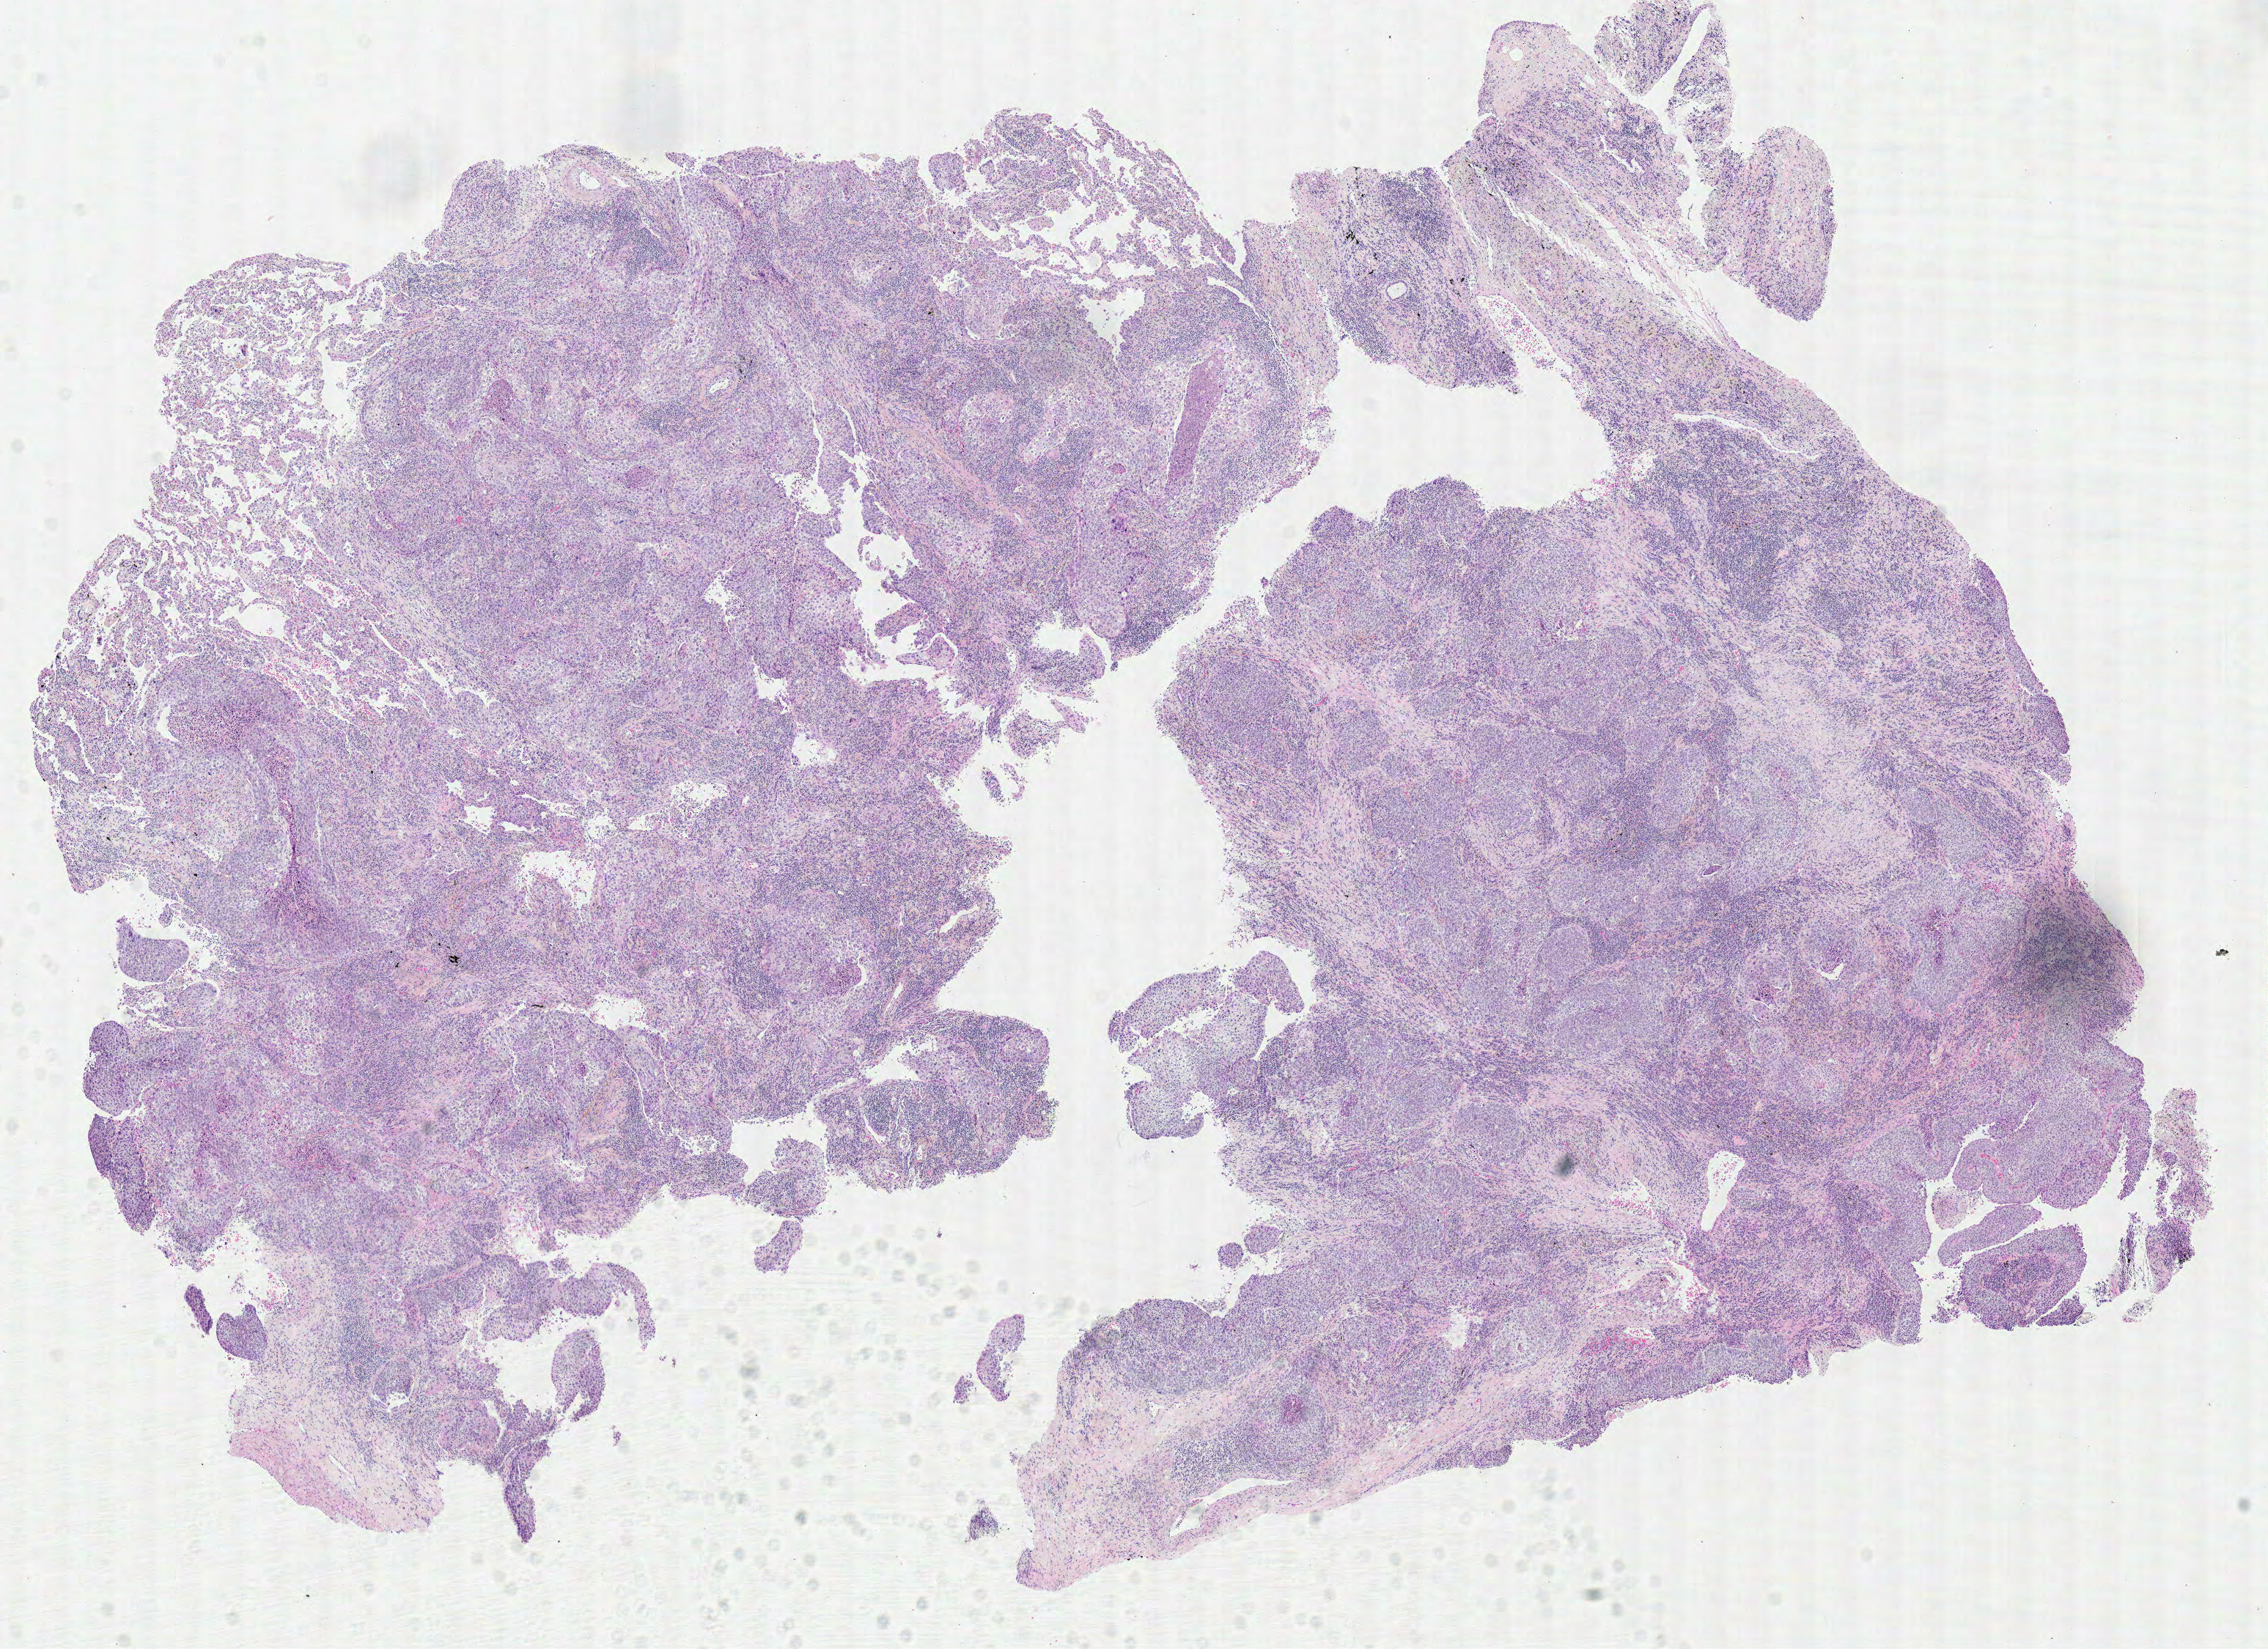
H&E whole-slide image, a low-resolution overview of the entire scanned area, about 12.2 x 8.9 mm. Formalin-fixed paraffin-embedded (FFPE) diagnostic section. Primary tumour sample from the lung. Male, age 60 years at initial diagnosis.
Histologic diagnosis: Squamous cell carcinoma, NOS (upper lobe, lung). TNM: T2 N1 M0. AJCC pathologic stage: IIB.